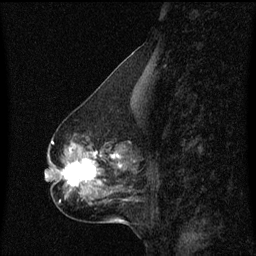
Breast MRI (dynamic contrast-enhanced), one sagittal slice. Position 25 of 60 along the scan axis. Dynamic contrast-enhanced series, image 2 of 3 at this slice position (ordered by acquisition). 1.5 T. TE 4.2 ms, TR 8.4 ms. 256 × 256 image matrix, field of view 200 × 200 mm. Female patient, age 50 years. Case-level facts recorded for this patient, not image findings: setting: breast cancer imaged before/during neoadjuvant chemotherapy; receptor status: HR-positive, HER2-negative.
Outlined on this slice (semi-automatic segmentation, software-assisted and operator-edited):
- analysis volume of interest (the breast-tissue region the enhancement analysis was run in; not a lesion): bounding box <55,140,133,191> (left, top, right, bottom; pixels)
- tumour enhancement mask (voxels above the 70 % enhancement threshold inside the analysis volume of interest): <63,148,123,187>